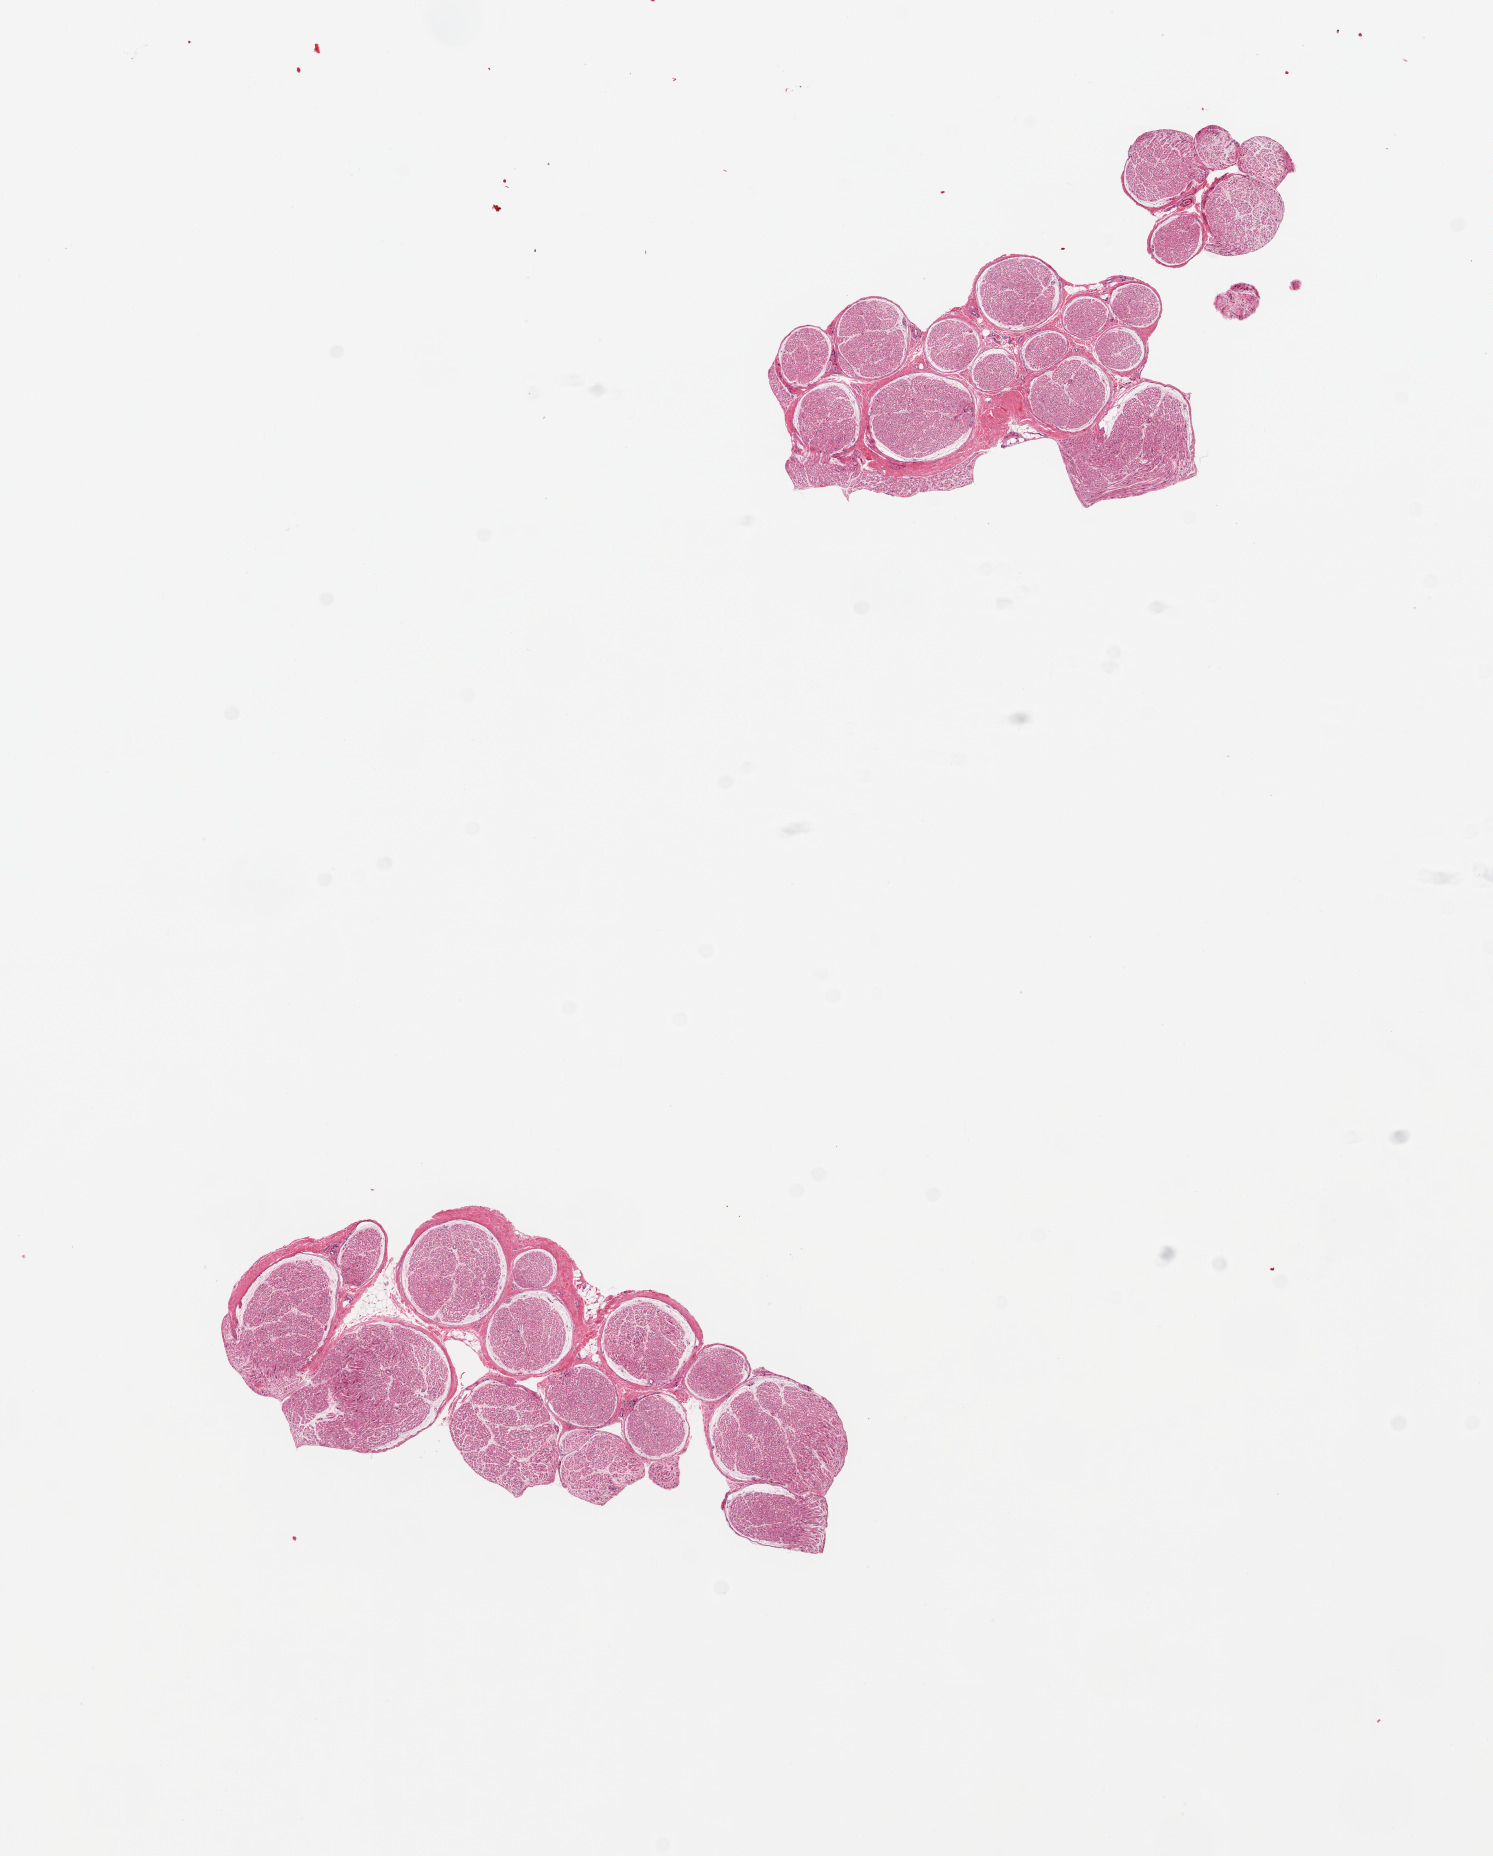
Digitized H&E-stained section, shown as a low-resolution overview of the whole scanned area (about 11.8 x 14.7 mm, from a 20x scan). PAXgene-fixed, paraffin-embedded tissue. Target tissue: tibial nerve. Tissue donor sample. Donor: female.
Pathologist's review note for this sample: 2 pieces; 5% internal fat in 1 piece.